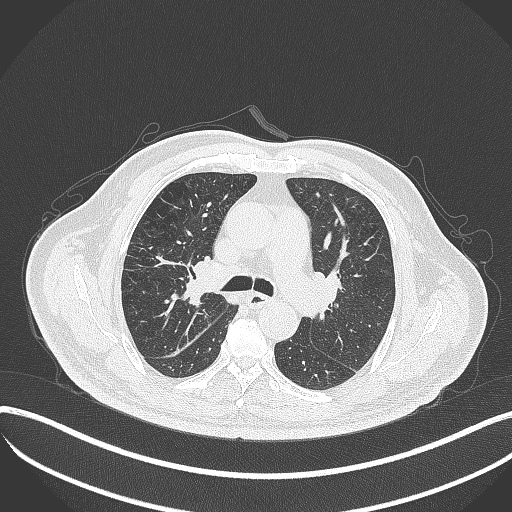
Chest CT, one axial slice; position 233 of 401 along the scan axis; 120 kVp; lung window (W 1500 / L -600 HU); 1 mm slice thickness; 512 × 512 image matrix, field of view 400 × 400 mm. Male patient, age 72 years. Case-level facts recorded for this patient, not image findings: clinical TNM (as recorded): T1c N0 M0; histopathological grade: G2.
Structures marked on this image (bounding box drawn by a radiologist):
- lung tumour (recorded histology: squamous cell carcinoma): bounding box (x1, y1, x2, y2) in pixels: (181, 262, 209, 311)